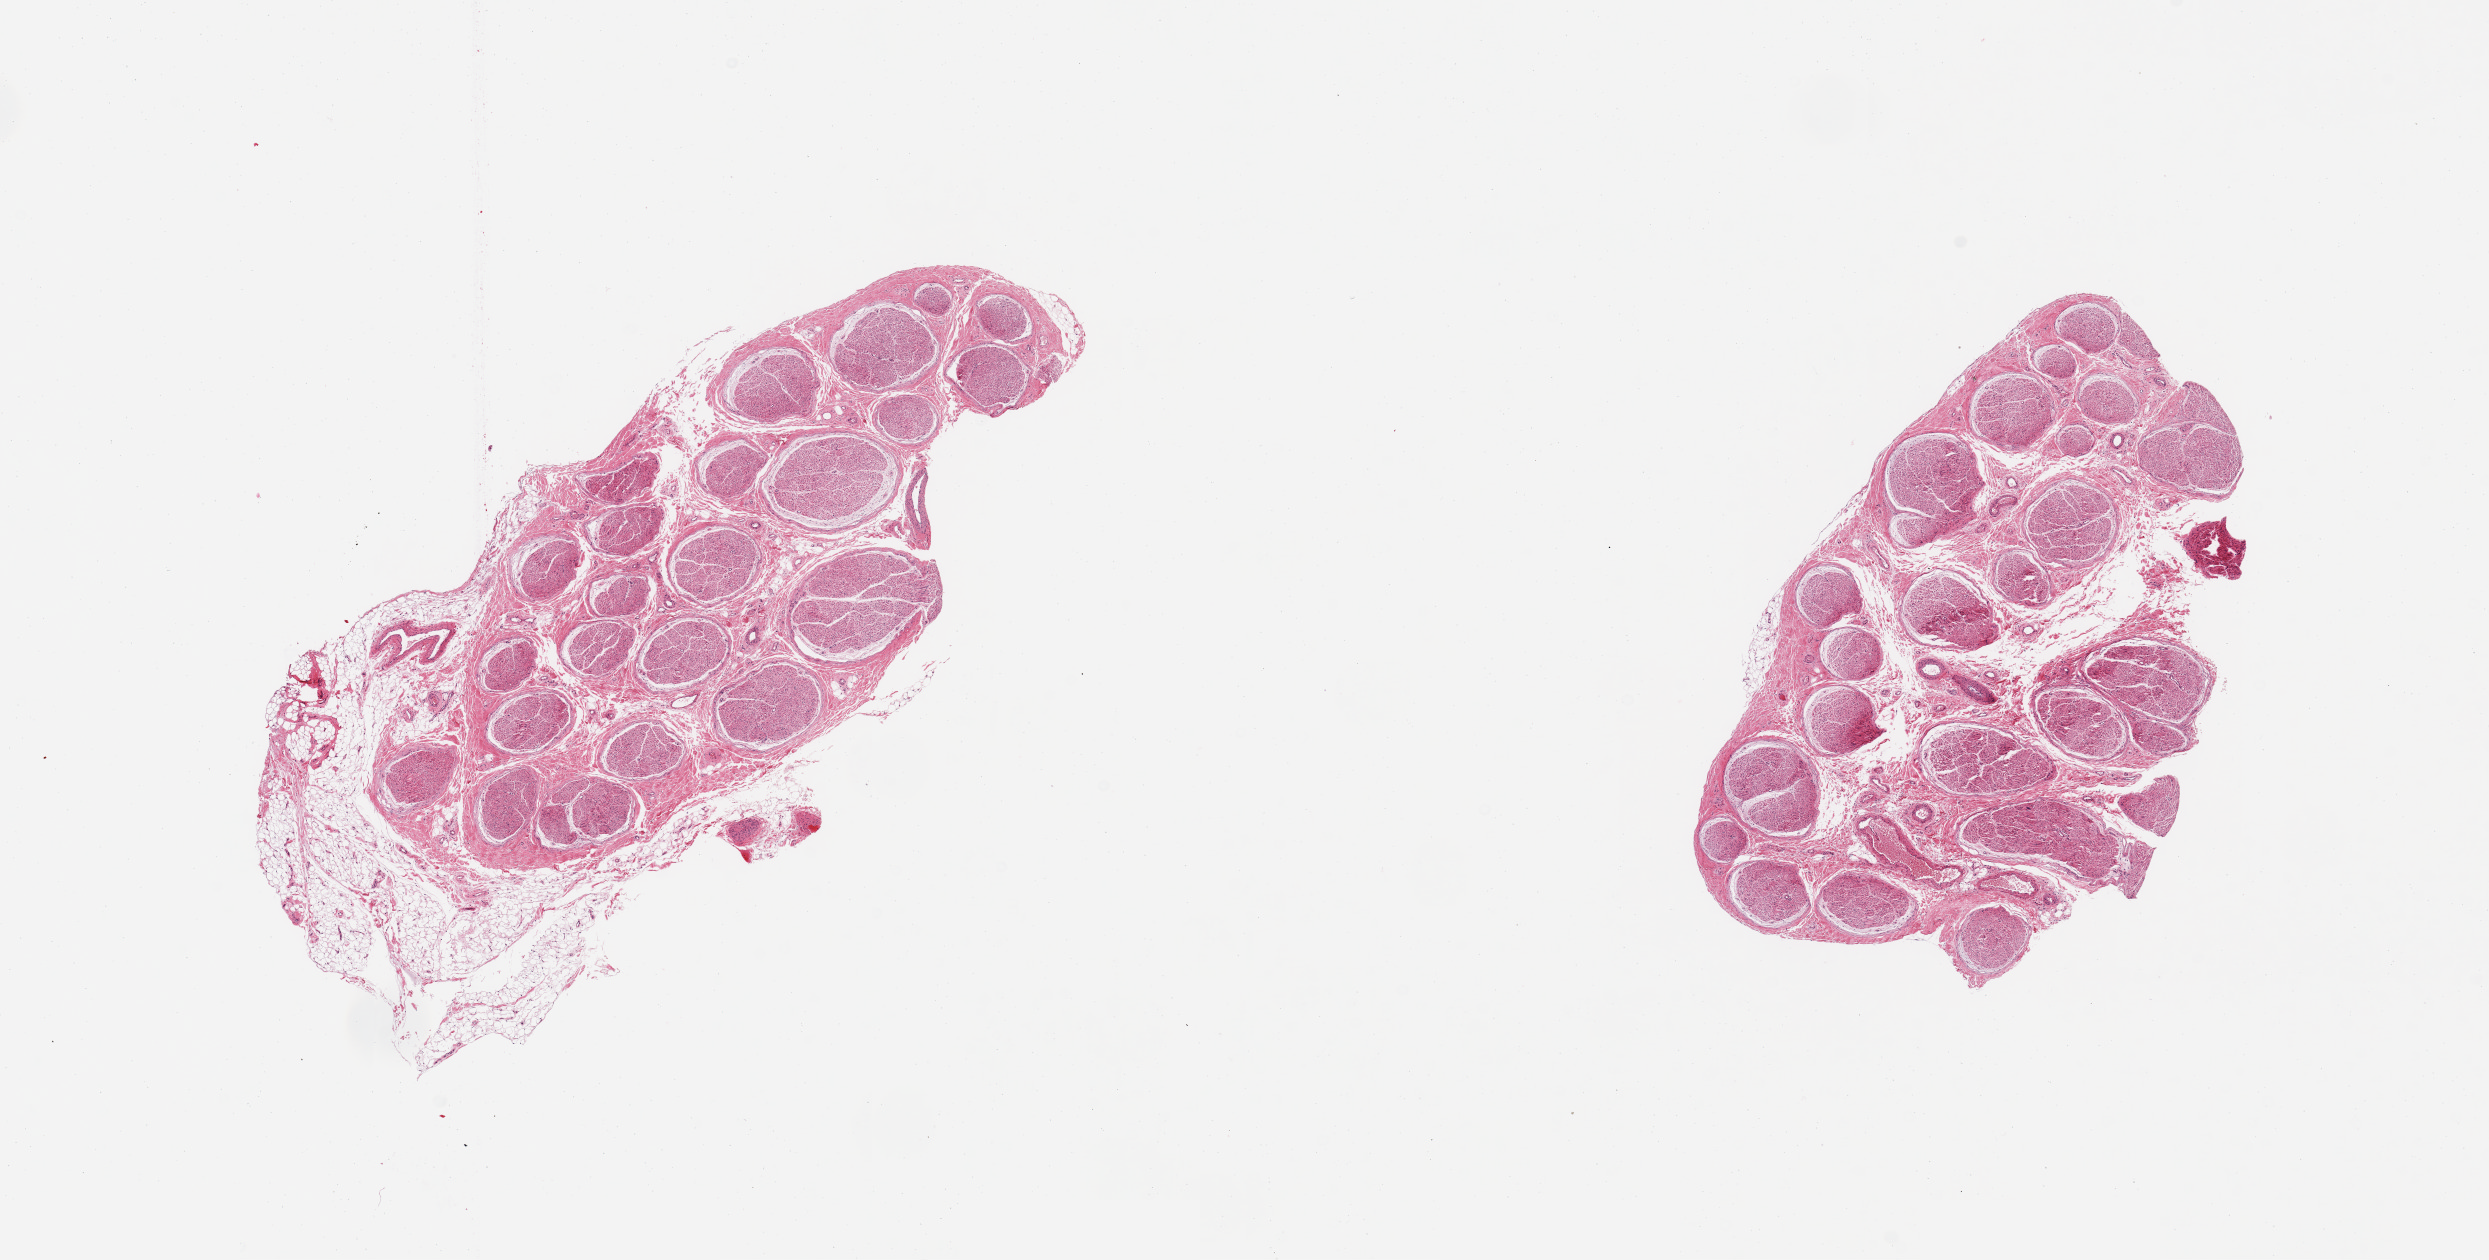
Digitized H&E-stained section, brightfield — low-resolution overview of the scanned area, about 19.7 x 10.0 mm (slide scanned at 20x), PAXgene-fixed paraffin-embedded (PFPE) section, section of tibial nerve (target tissue), donor tissue sample. Donor sex: male.
• review note (as recorded): 2 pieces; 1 with no external fat; other with 20% external fat